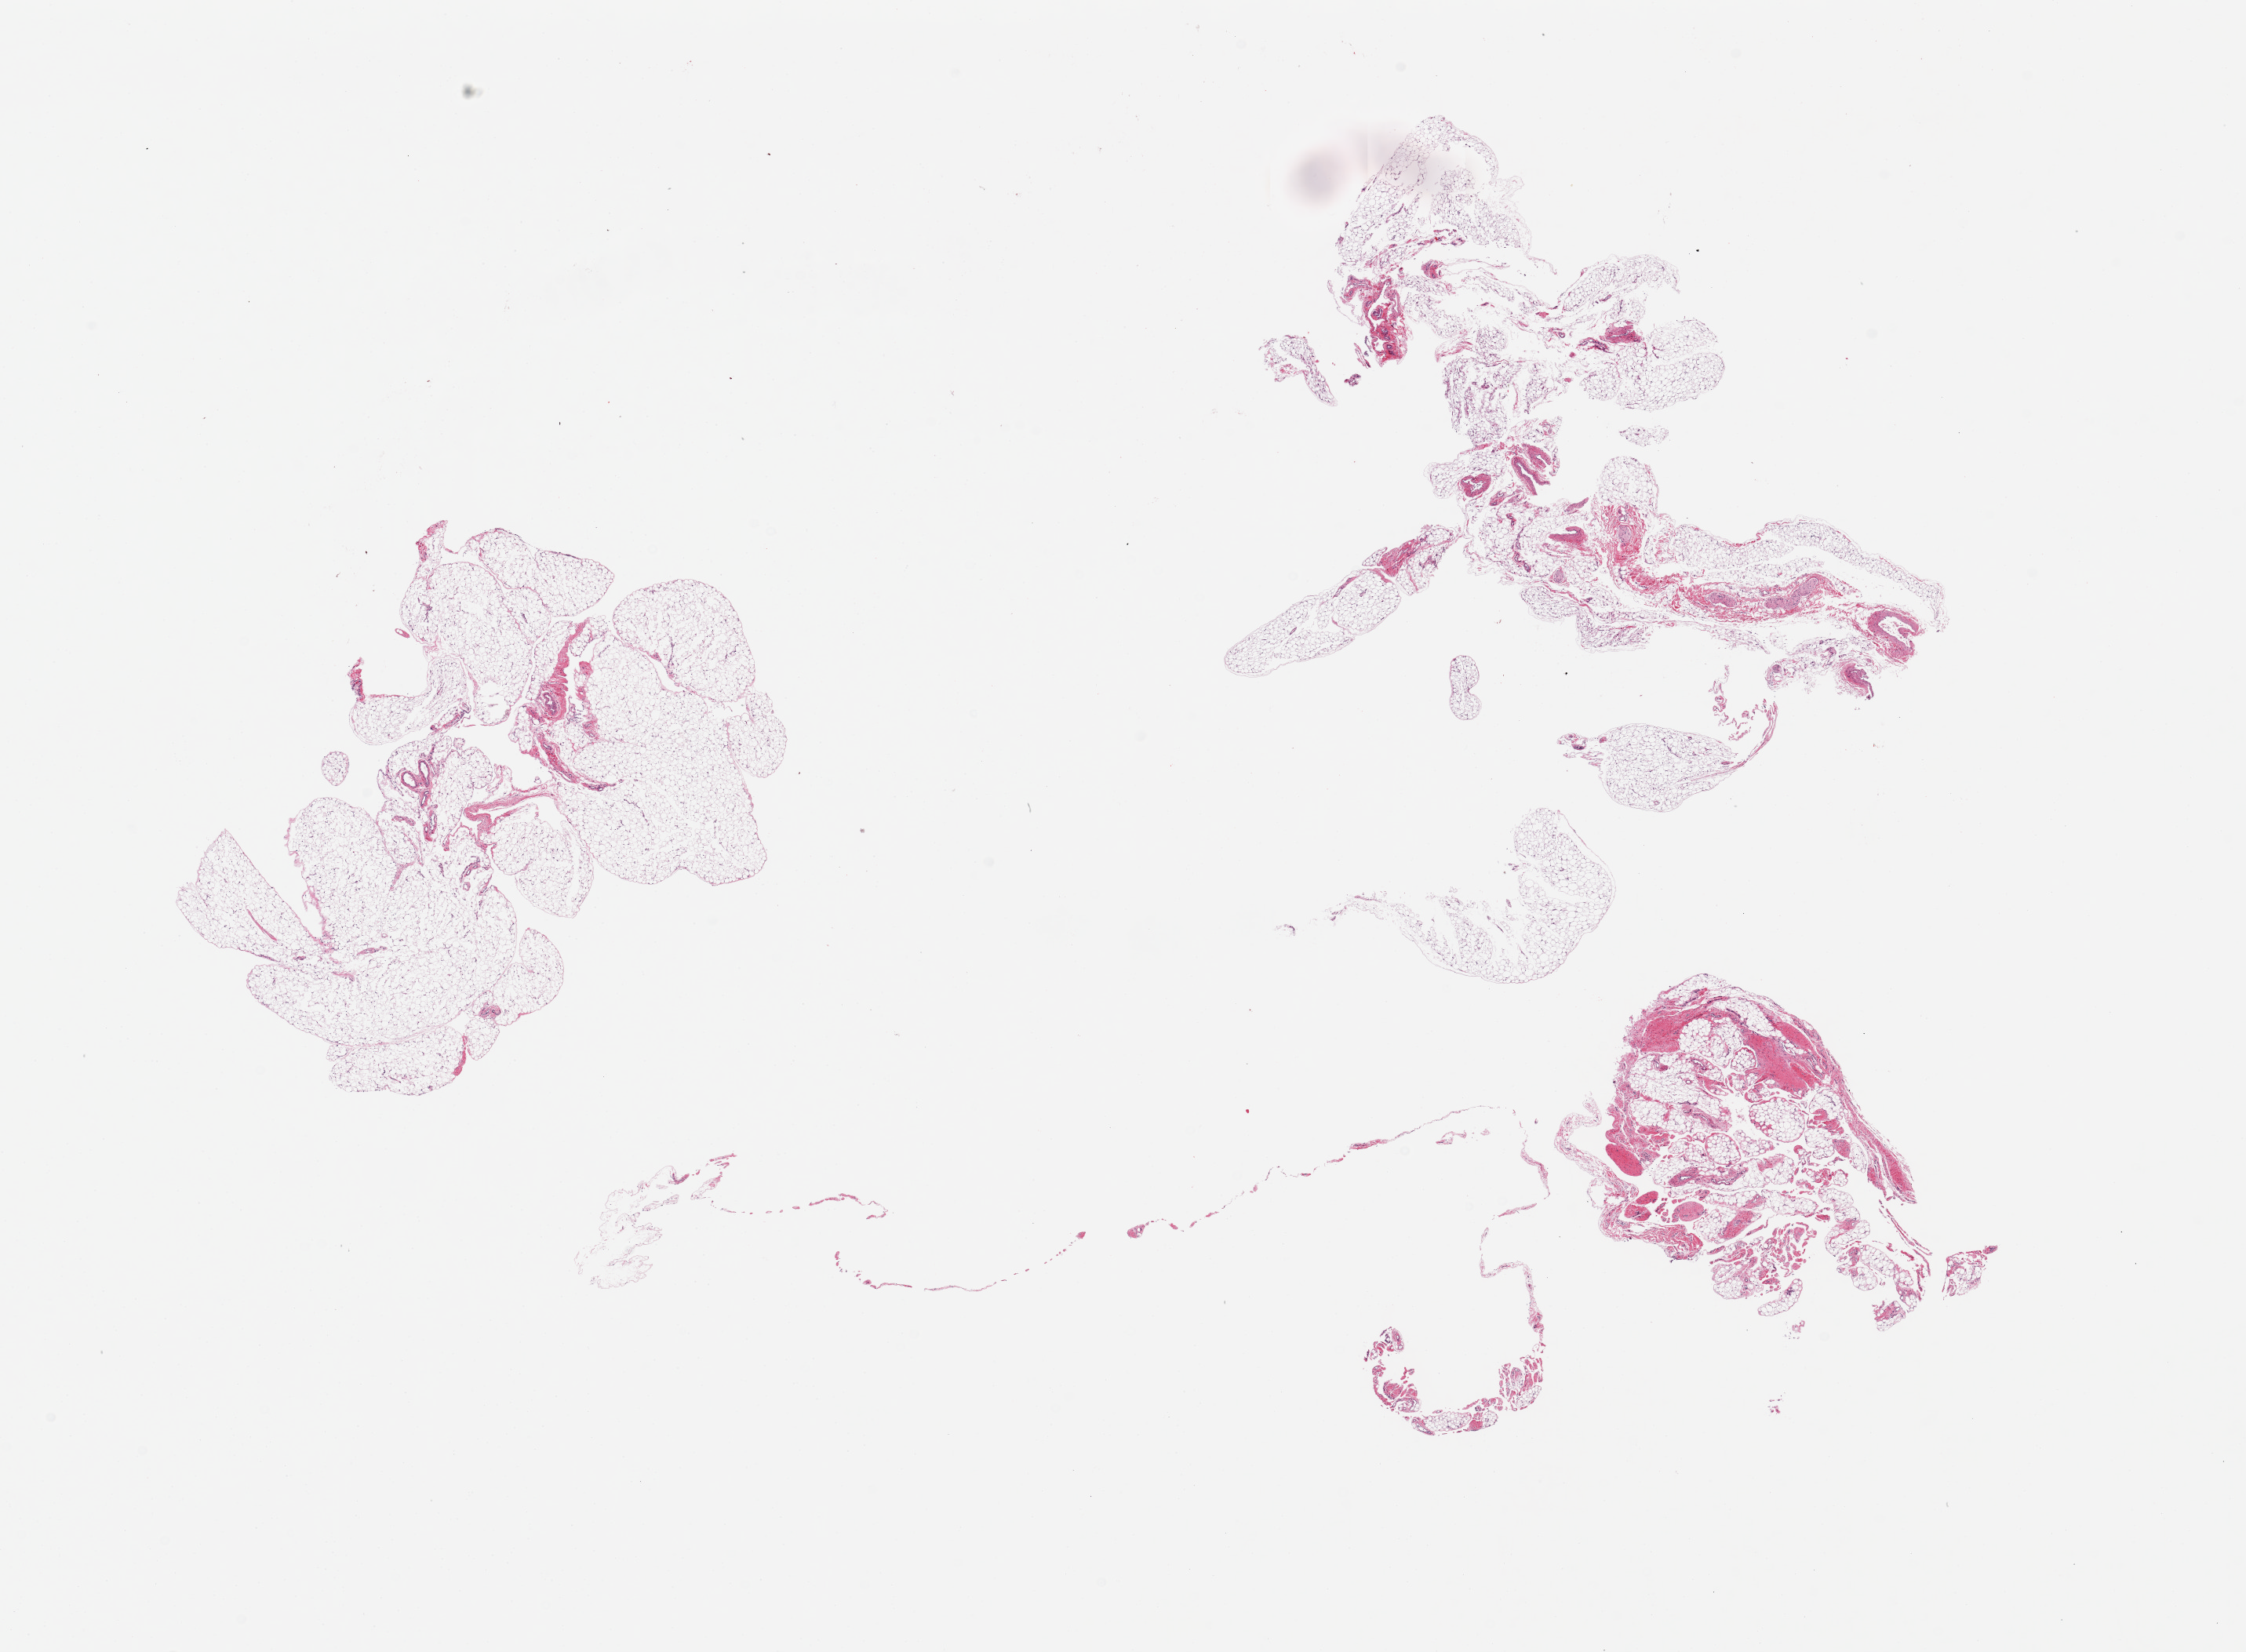
H&E whole-slide image, whole scanned area (about 22.6 x 16.7 mm) shown as a low-resolution overview; PAXgene-fixed, paraffin-embedded tissue; section of omentum (target tissue); donor tissue sample. Male donor.
Review note (as recorded): 3 pieces, up to 7x7mm; lobulated structure; 1 with 10% neurovascular elements.